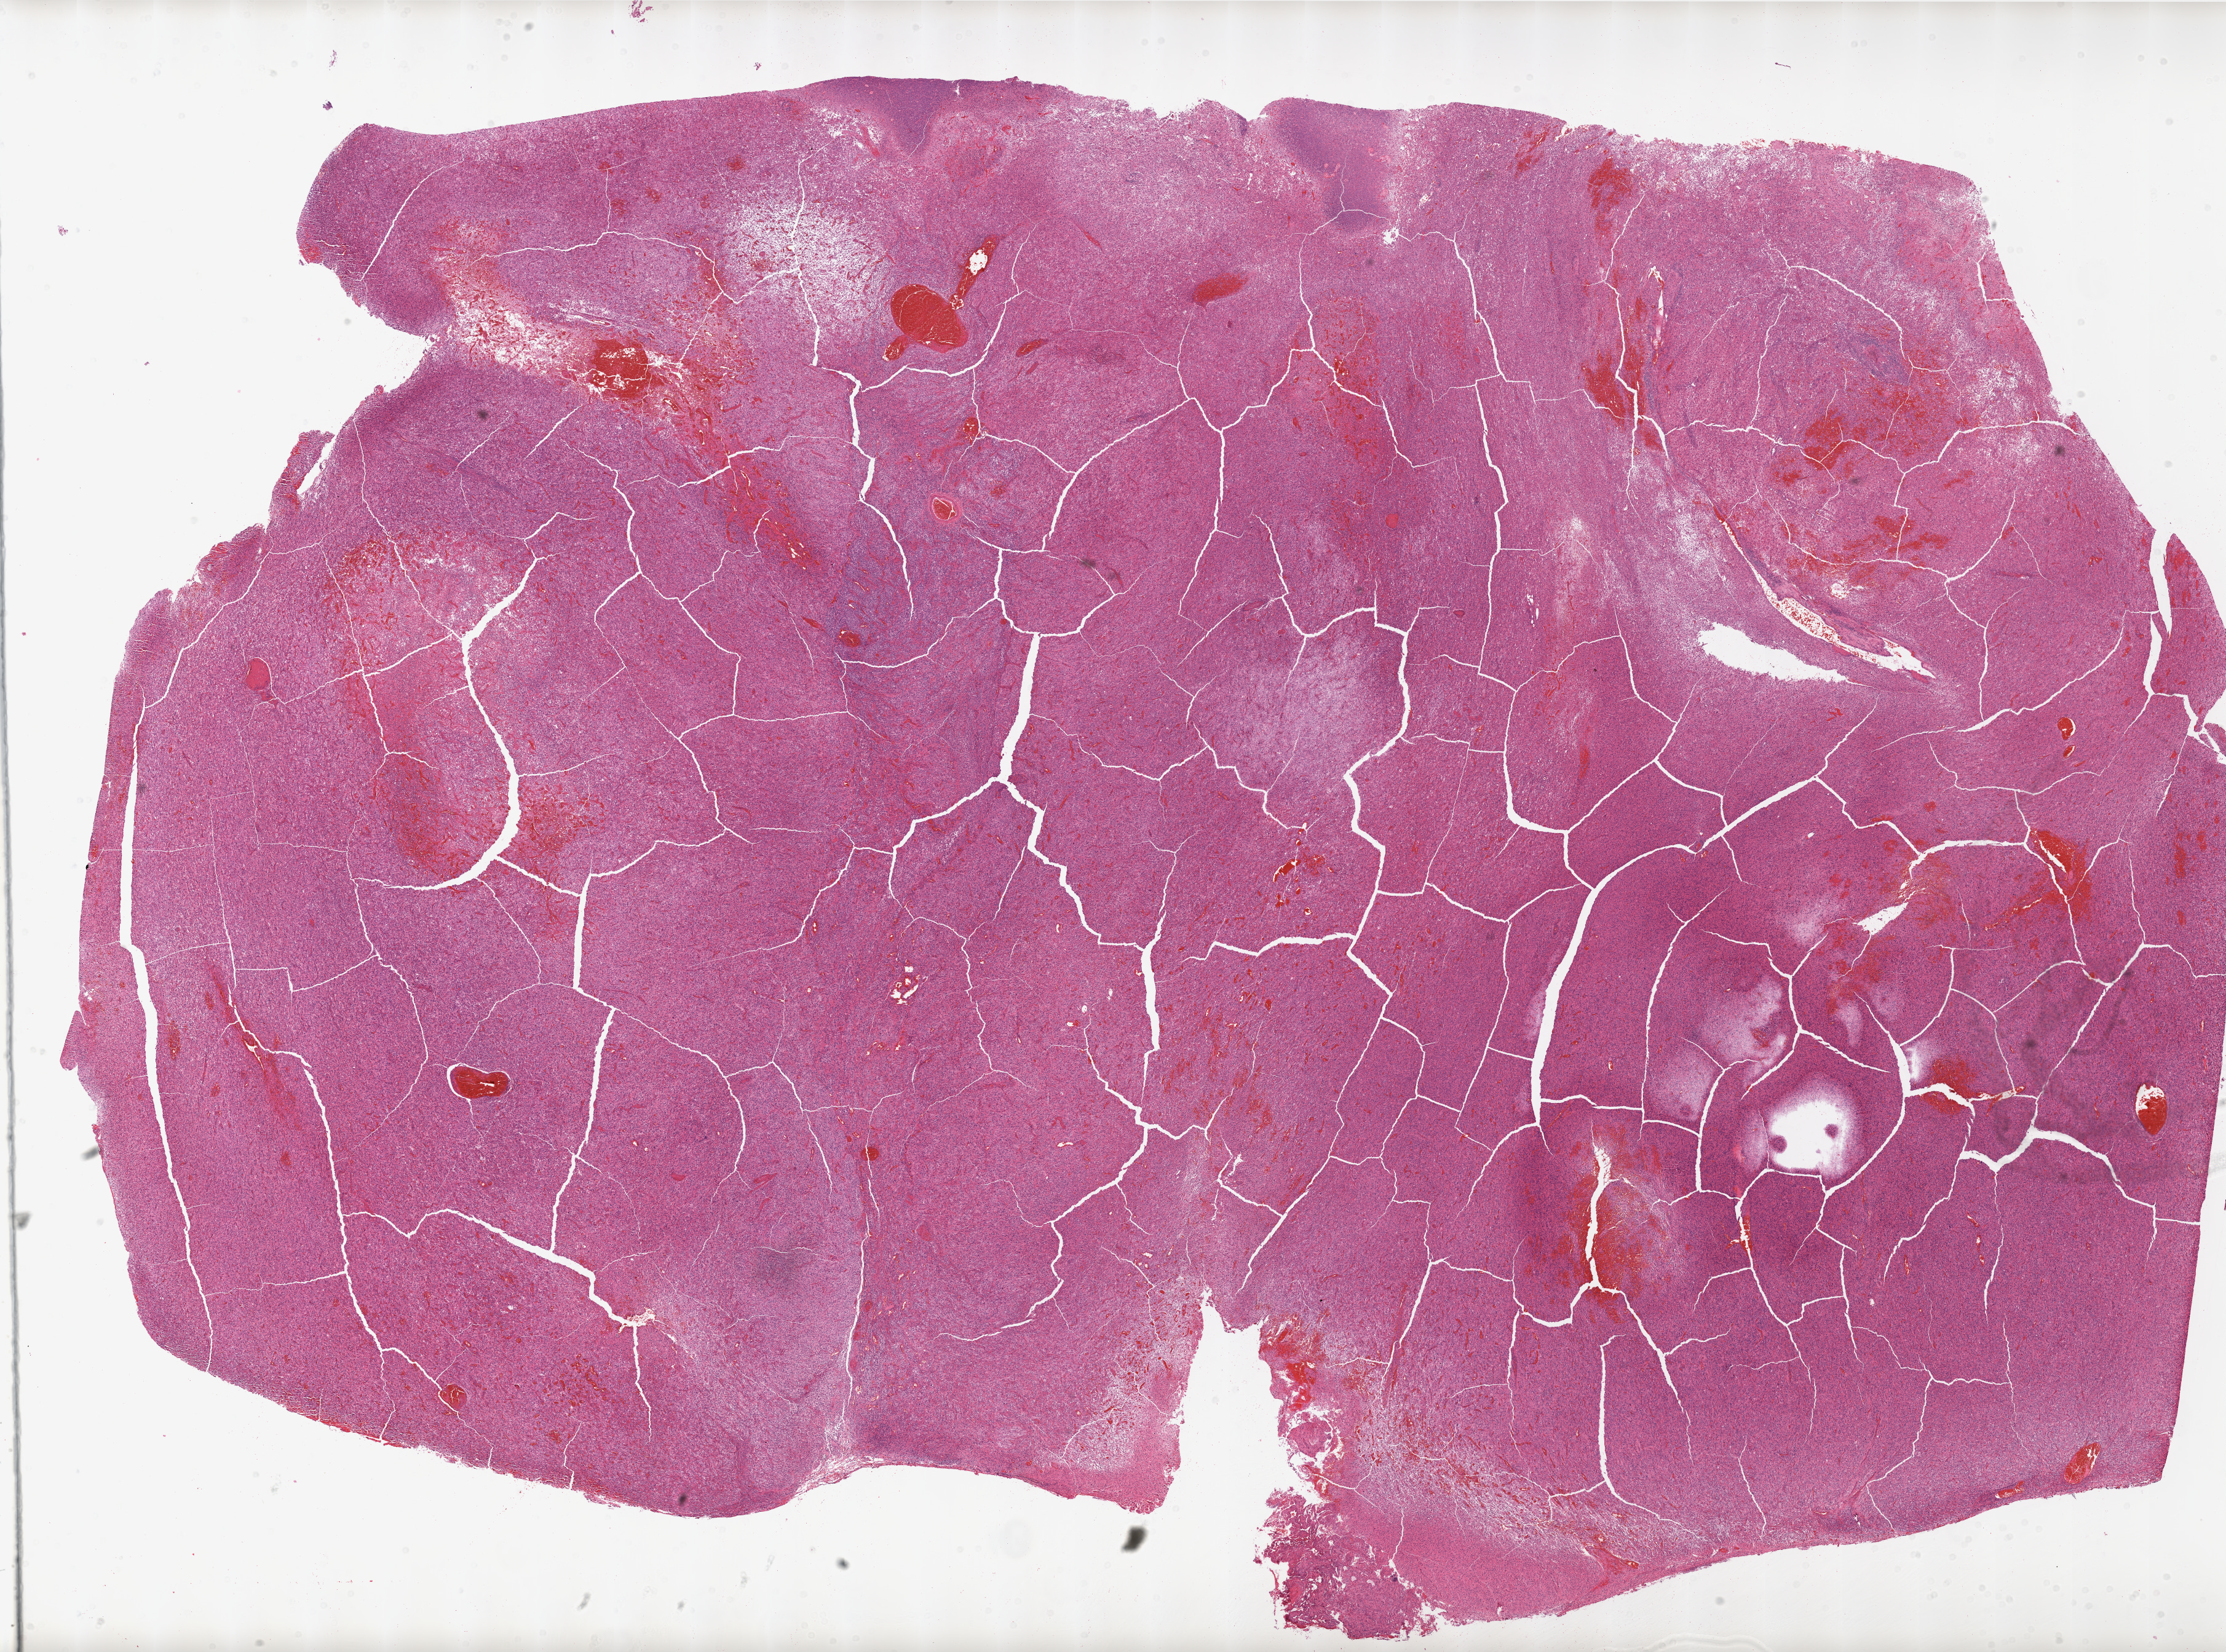
Whole-slide histology image, H&E-stained — shown as a low-resolution overview of the whole scanned area (about 29.0 x 21.5 mm); formalin-fixed paraffin-embedded (FFPE) diagnostic section; sample: primary tumour, brain. Female, age 52 years at initial diagnosis.
Diagnosis: Glioblastoma.